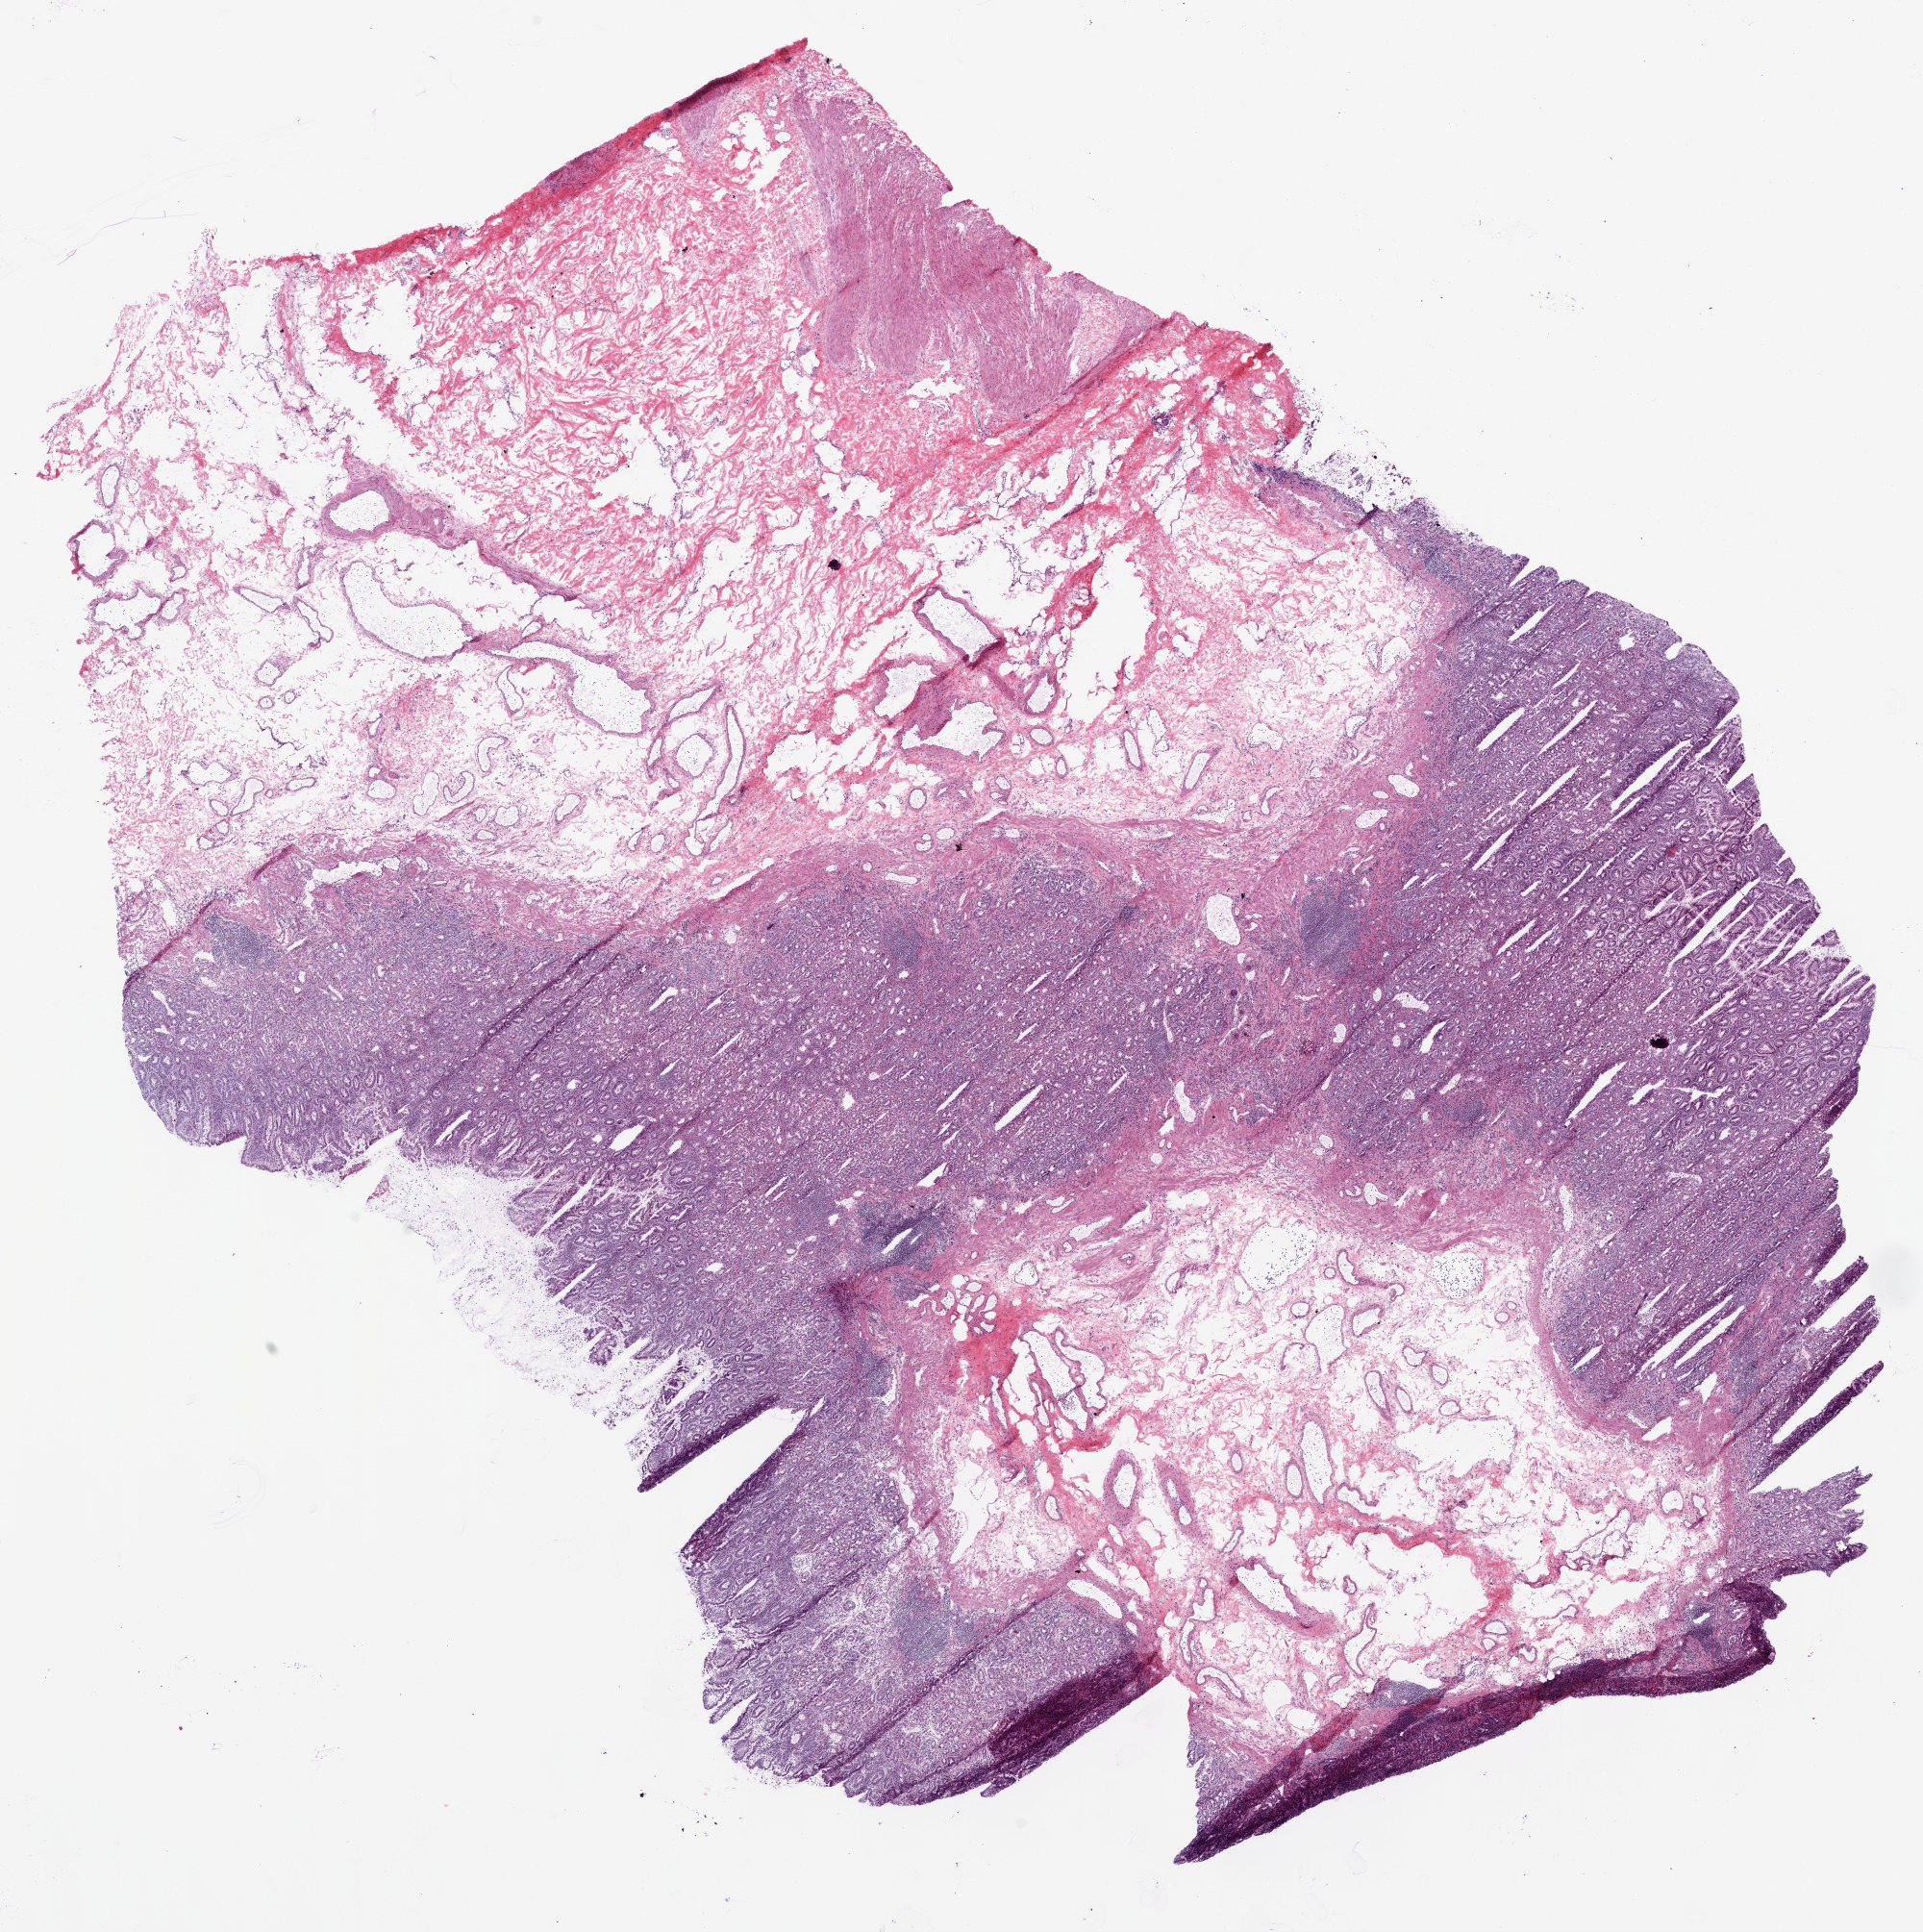
Digitized H&E-stained tissue section (whole slide), shown as a low-resolution overview of the whole scanned area (about 16.0 x 16.1 mm, acquisition: 20x scan); frozen section from the bottom of the tissue portion; sample: solid tissue normal (non-tumour tissue), stomach. Female, age 66 years at initial diagnosis.
• this section: solid tissue normal sample (biorepository sample class)
• patient diagnosis: Adenocarcinoma, NOS